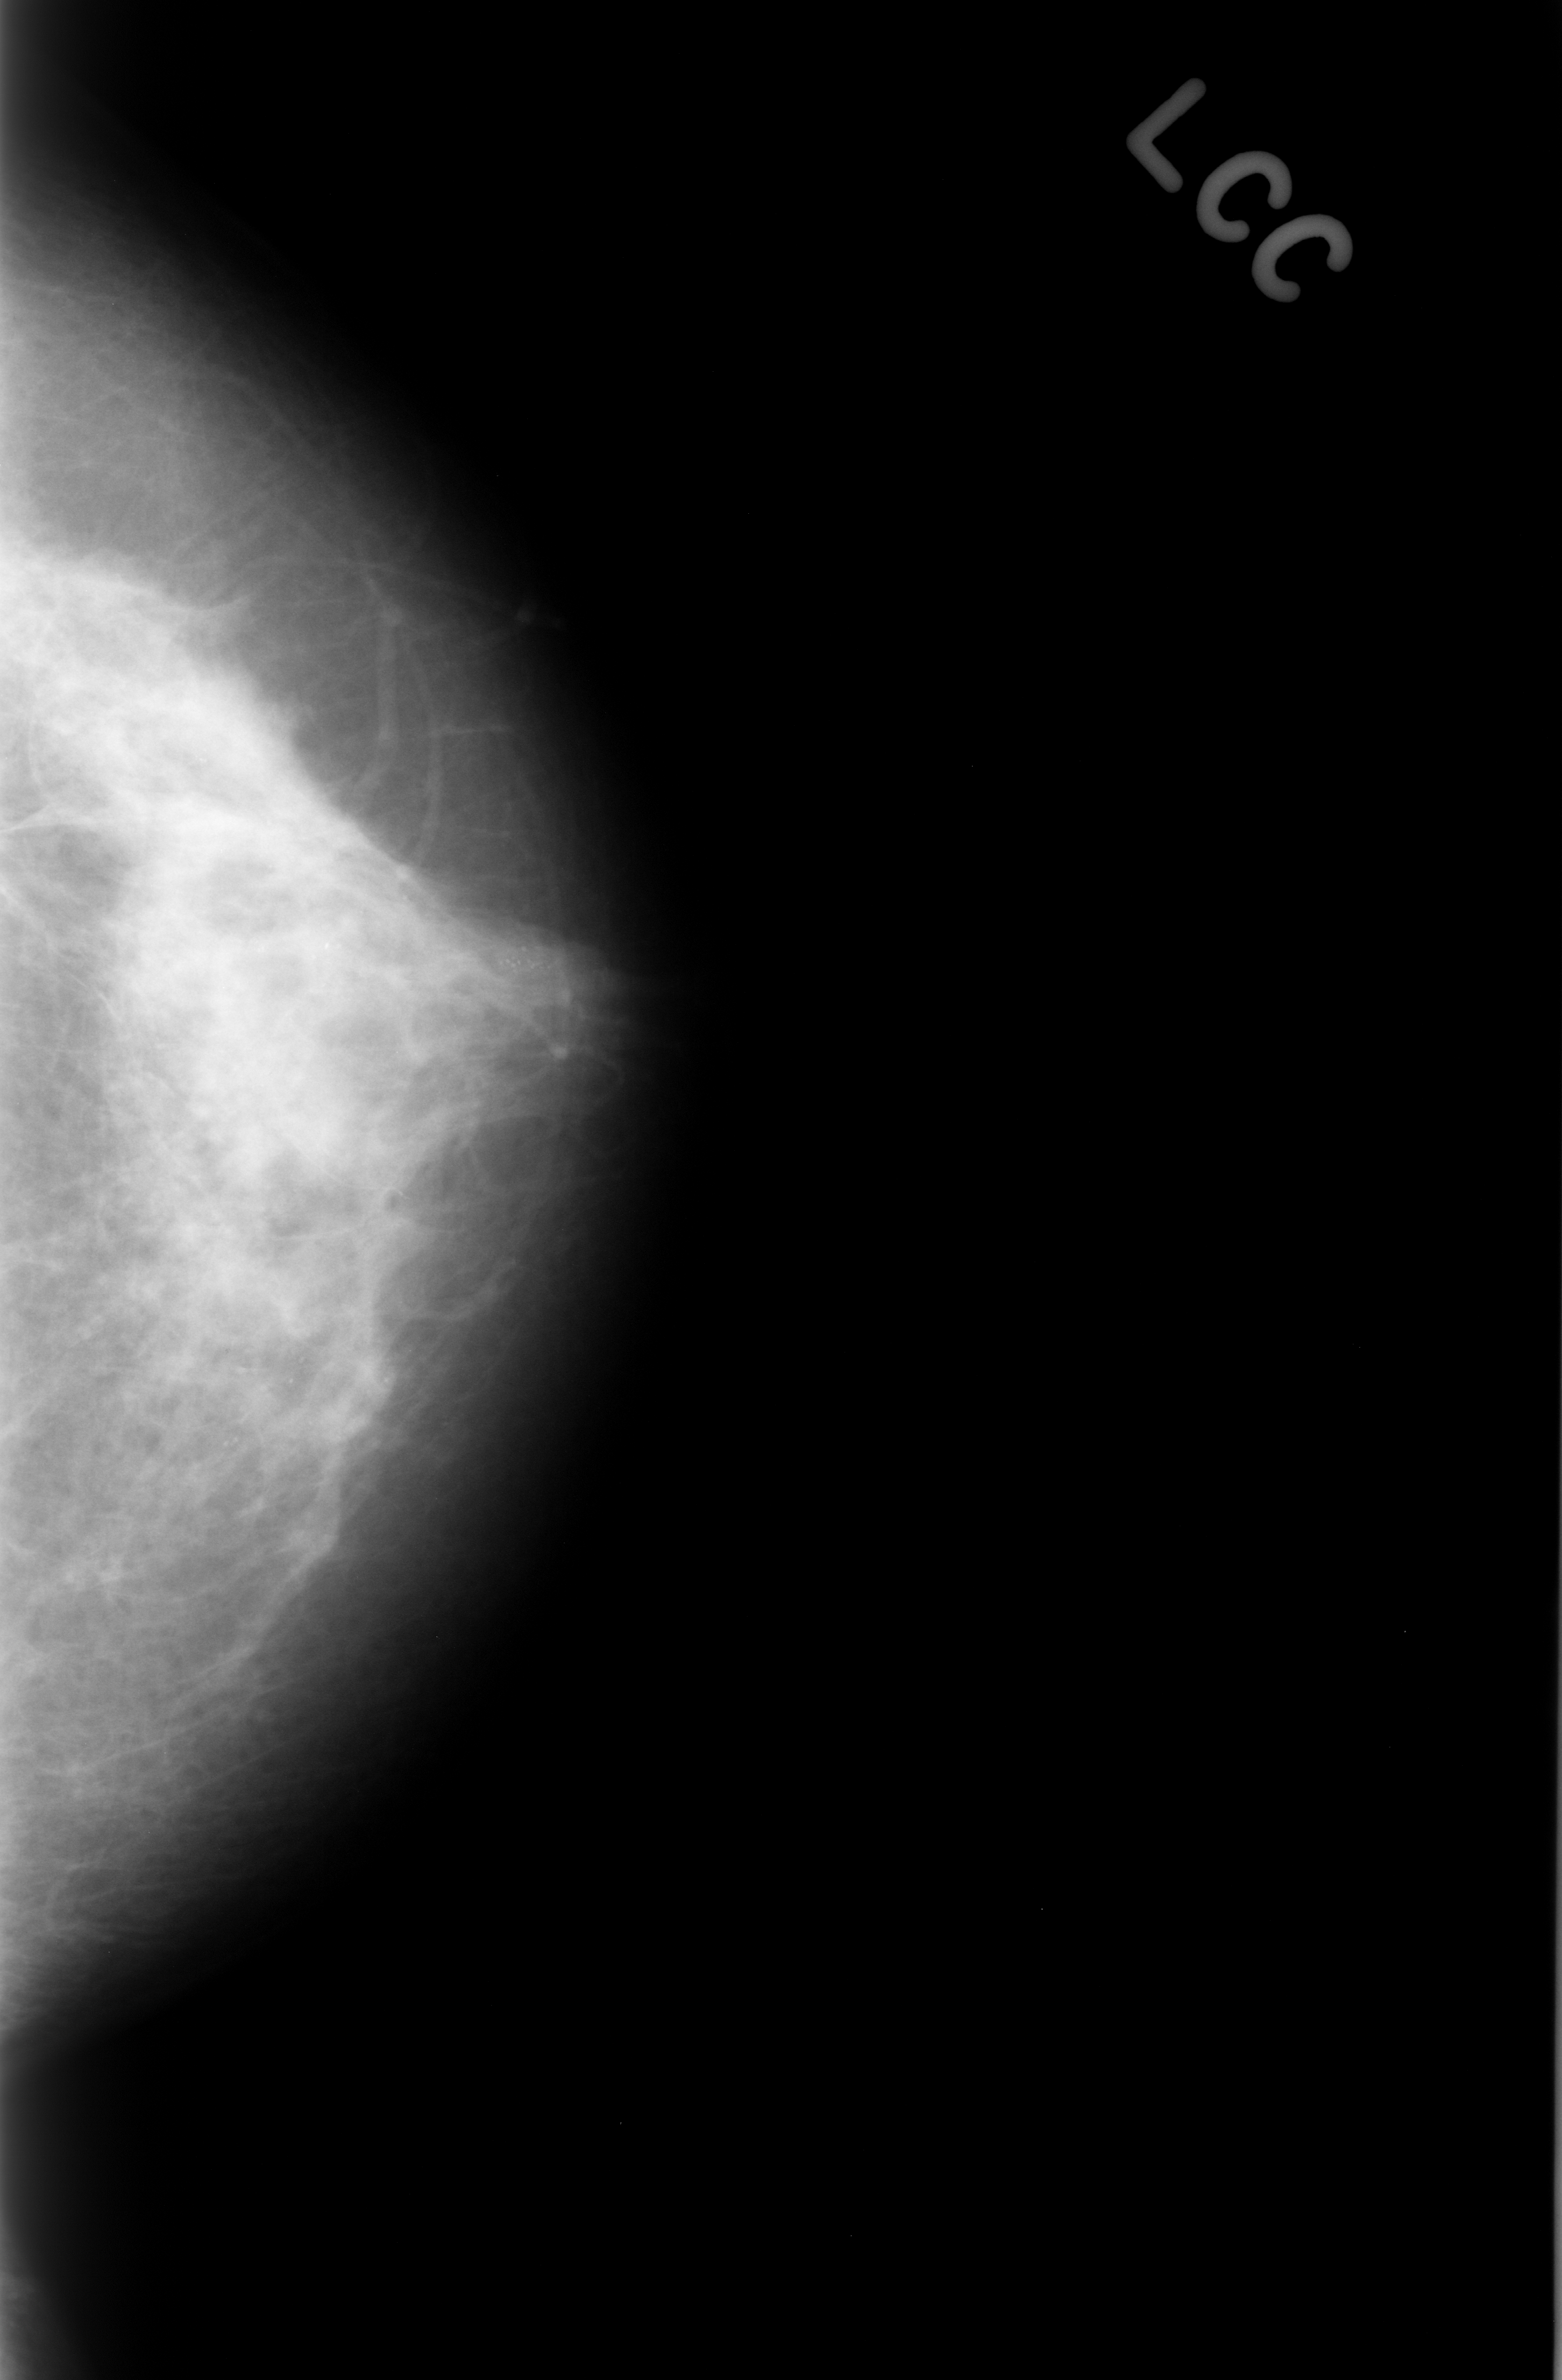
Mammogram (digitized film), left breast, craniocaudal (CC) view, BI-RADS breast density category 3 (scale 1–4).
- Marked abnormality: calcifications, morphology punctate, distribution clustered; BI-RADS assessment category 4; subtlety rating 3 on a 1 (subtle) to 5 (obvious) scale; pathology result (as recorded, not read from the image): benign.